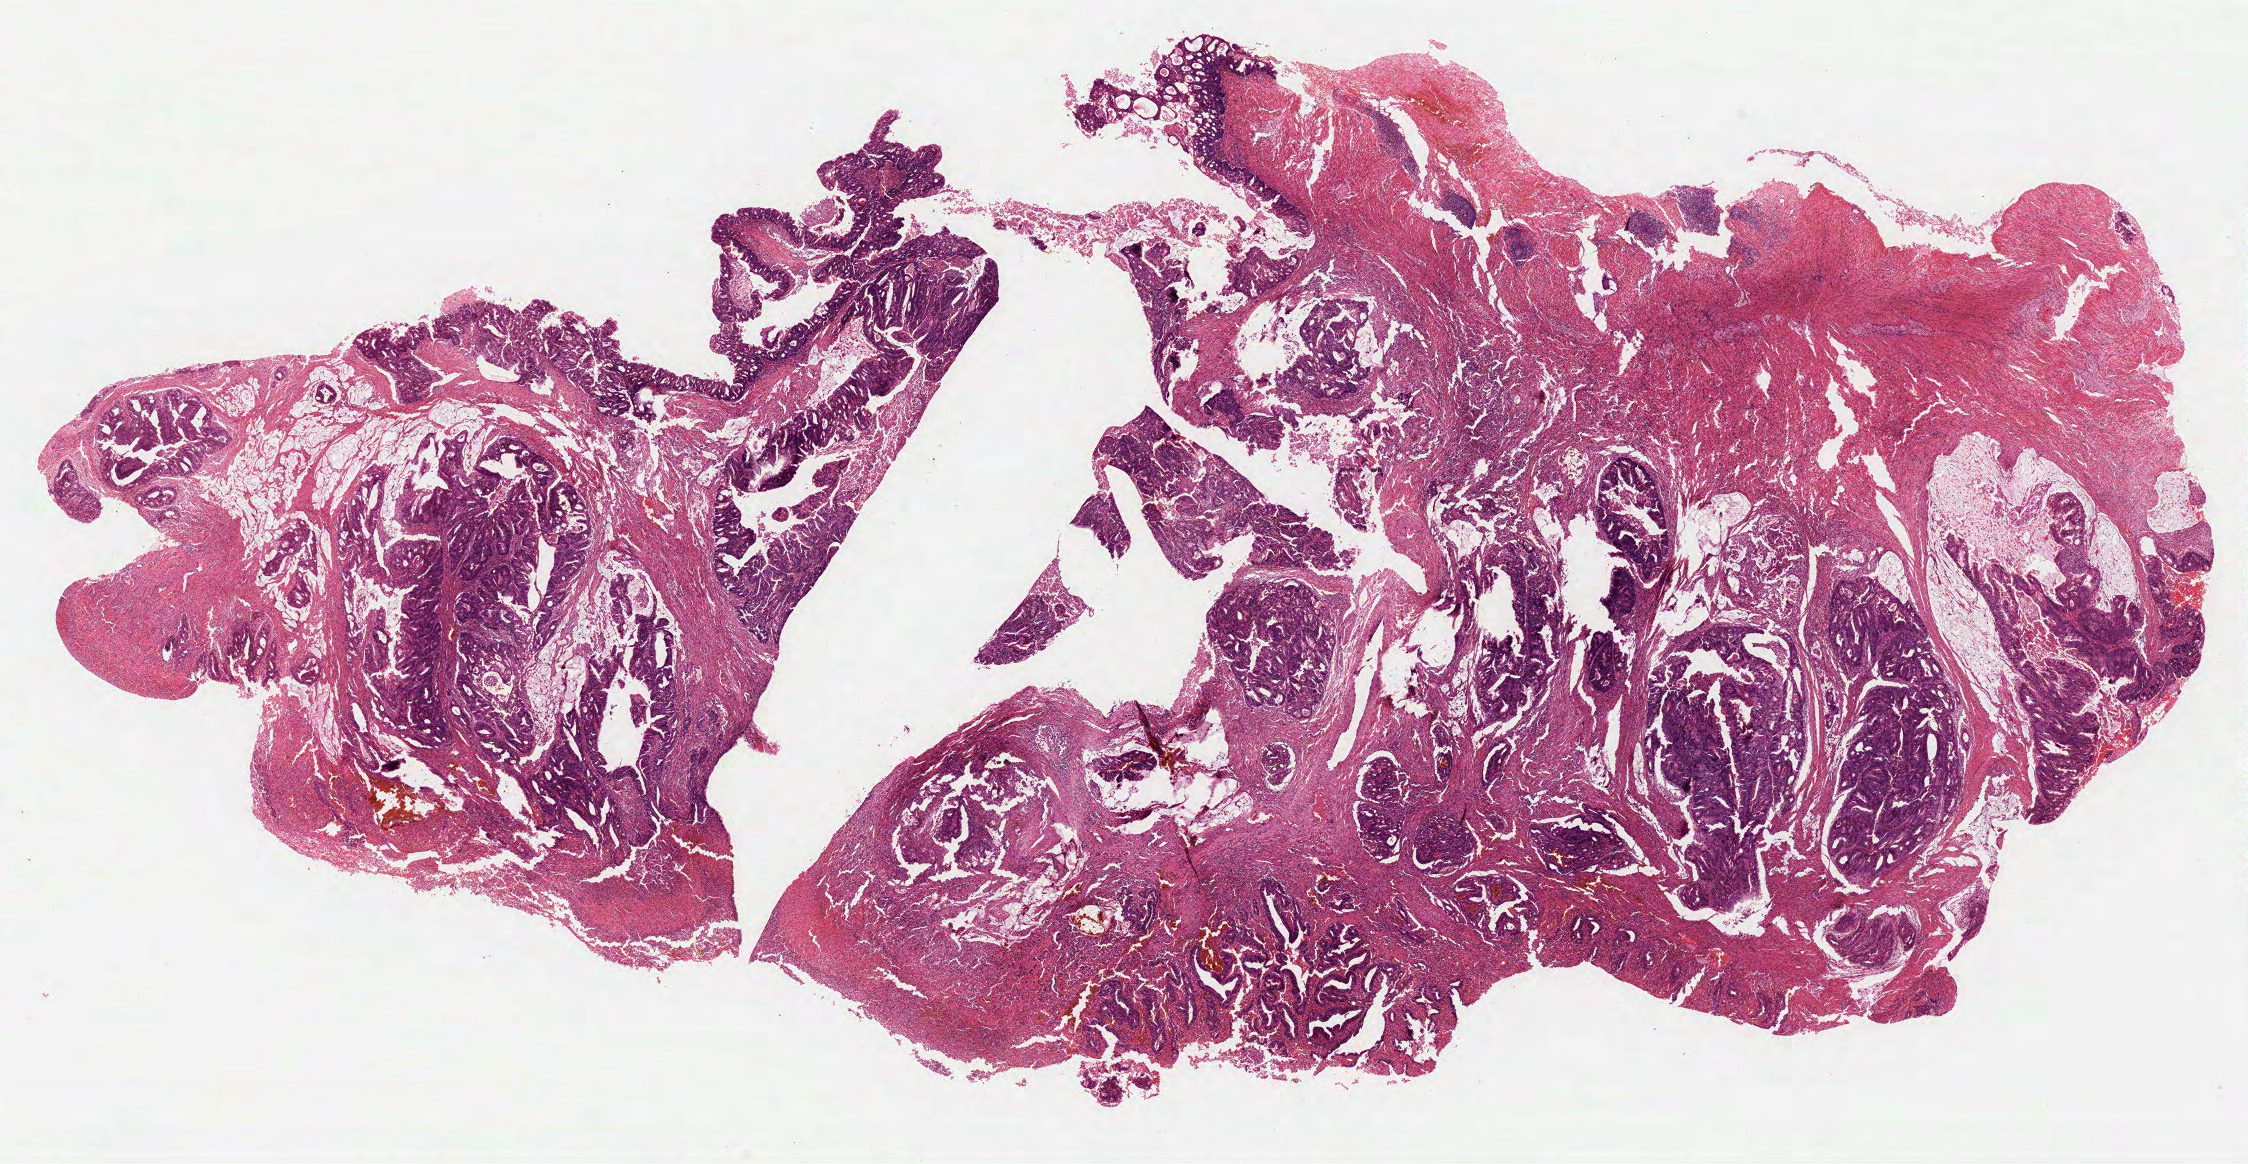
Whole-slide histology image, H&E, a low-resolution overview of the entire scanned area, about 18.1 x 9.4 mm (slide scanned at 40x); formalin-fixed paraffin-embedded (FFPE) diagnostic section; sample: primary tumour, colon. Patient: male, age at initial diagnosis 51 years.
AJCC pathologic stage: IIA (7th edition). Diagnosis: Mucinous adenocarcinoma (transverse colon). Lymph nodes positive (case pathology): 0 of 18 examined.